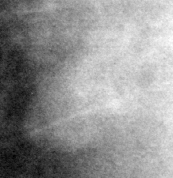
Cropped region of a digitized screen-film mammogram centred on a radiologist-marked abnormality, right breast, MLO view, BI-RADS breast density category 2 (scale 1–4).
- Mass, shape lobulated, margins microlobulated; BI-RADS assessment category 3; subtlety rating 4 on a 1 (subtle) to 5 (obvious) scale; benign without callback (not worked up further).